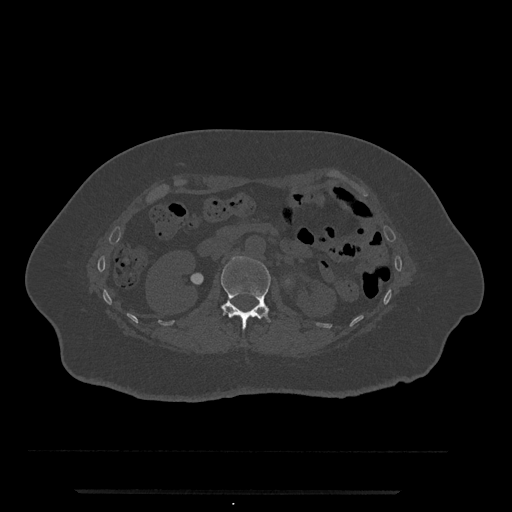
CT including the spine, one axial slice. Slice 100 of 797 in the series (ordered by position). 120 kVp. Bone window (W 1800 / L 400 HU). 0.5 mm slice thickness. 512 × 512 image matrix, field of view 440 × 440 mm. Patient: female, 51 years. Case-level facts recorded for this patient, not image findings: primary cancer: neuro; vertebrae with lytic lesions (as recorded): T8.
Annotated regions visible in this slice (semi-automatically segmented with operator editing):
- L1 vertebra: box from (x=221, y=256) to (x=271, y=330) px